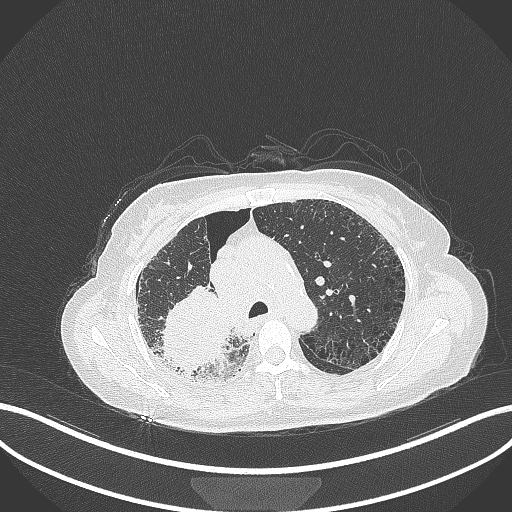
Chest CT, one axial slice; slice 241 of 408 in the series (ordered by position); reconstruction kernel B70f; lung window (W 1500 / L -600 HU); 512 × 512 image matrix, field of view 400 × 400 mm. Female patient, age 64 years. From the clinical record (not read from this slice): clinical TNM (as recorded): T3 N3 M0.
Structures marked on this image (bounding box drawn by a radiologist):
- lung tumour (recorded histology: squamous cell carcinoma): box from (x=159, y=283) to (x=231, y=378) px